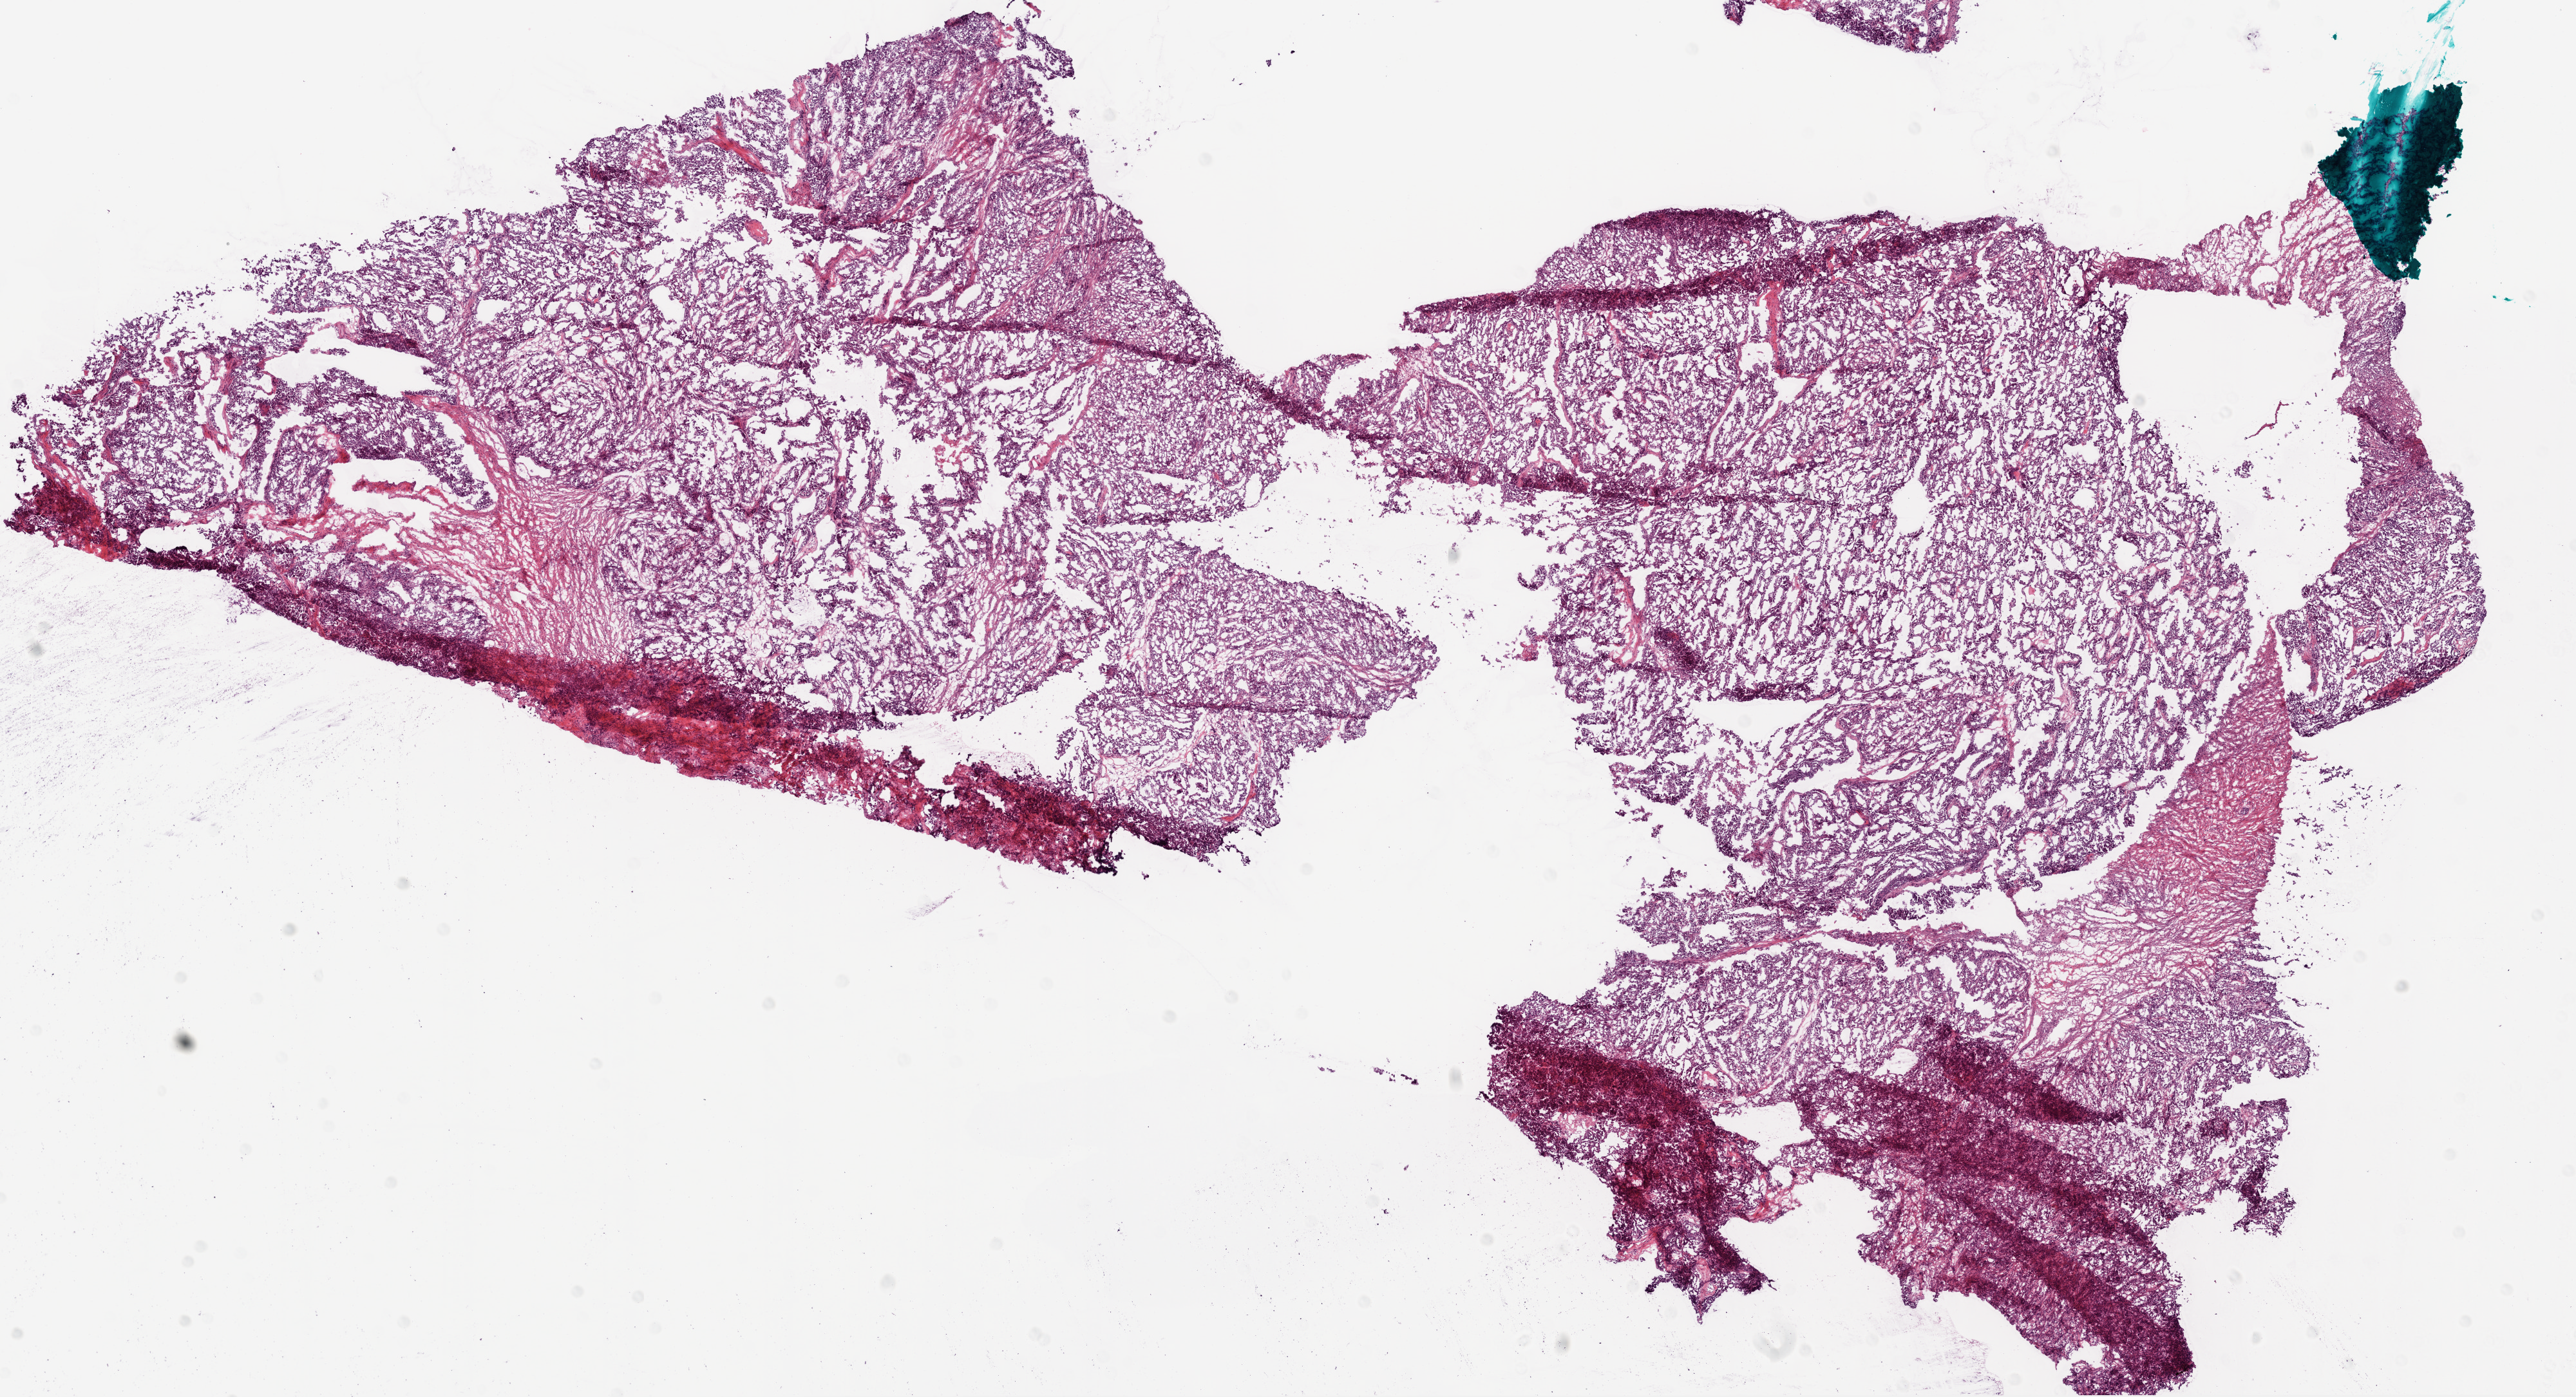
Whole-slide histology image, H&E-stained — shown as a low-resolution overview of the whole scanned area (about 16.0 x 8.7 mm, slide scanned at 20x); frozen section from the bottom of the tissue portion; ovary, primary tumour sample. Patient: female, age at initial diagnosis 60 years. Histologic grade: G3 (poorly differentiated). Slide review estimates, as recorded: tumour cells 85%, tumour nuclei 70%, normal cells 10%, stromal cells 0%, necrosis 5%.
Histologic diagnosis: Serous cystadenocarcinoma, NOS. FIGO stage: IV.